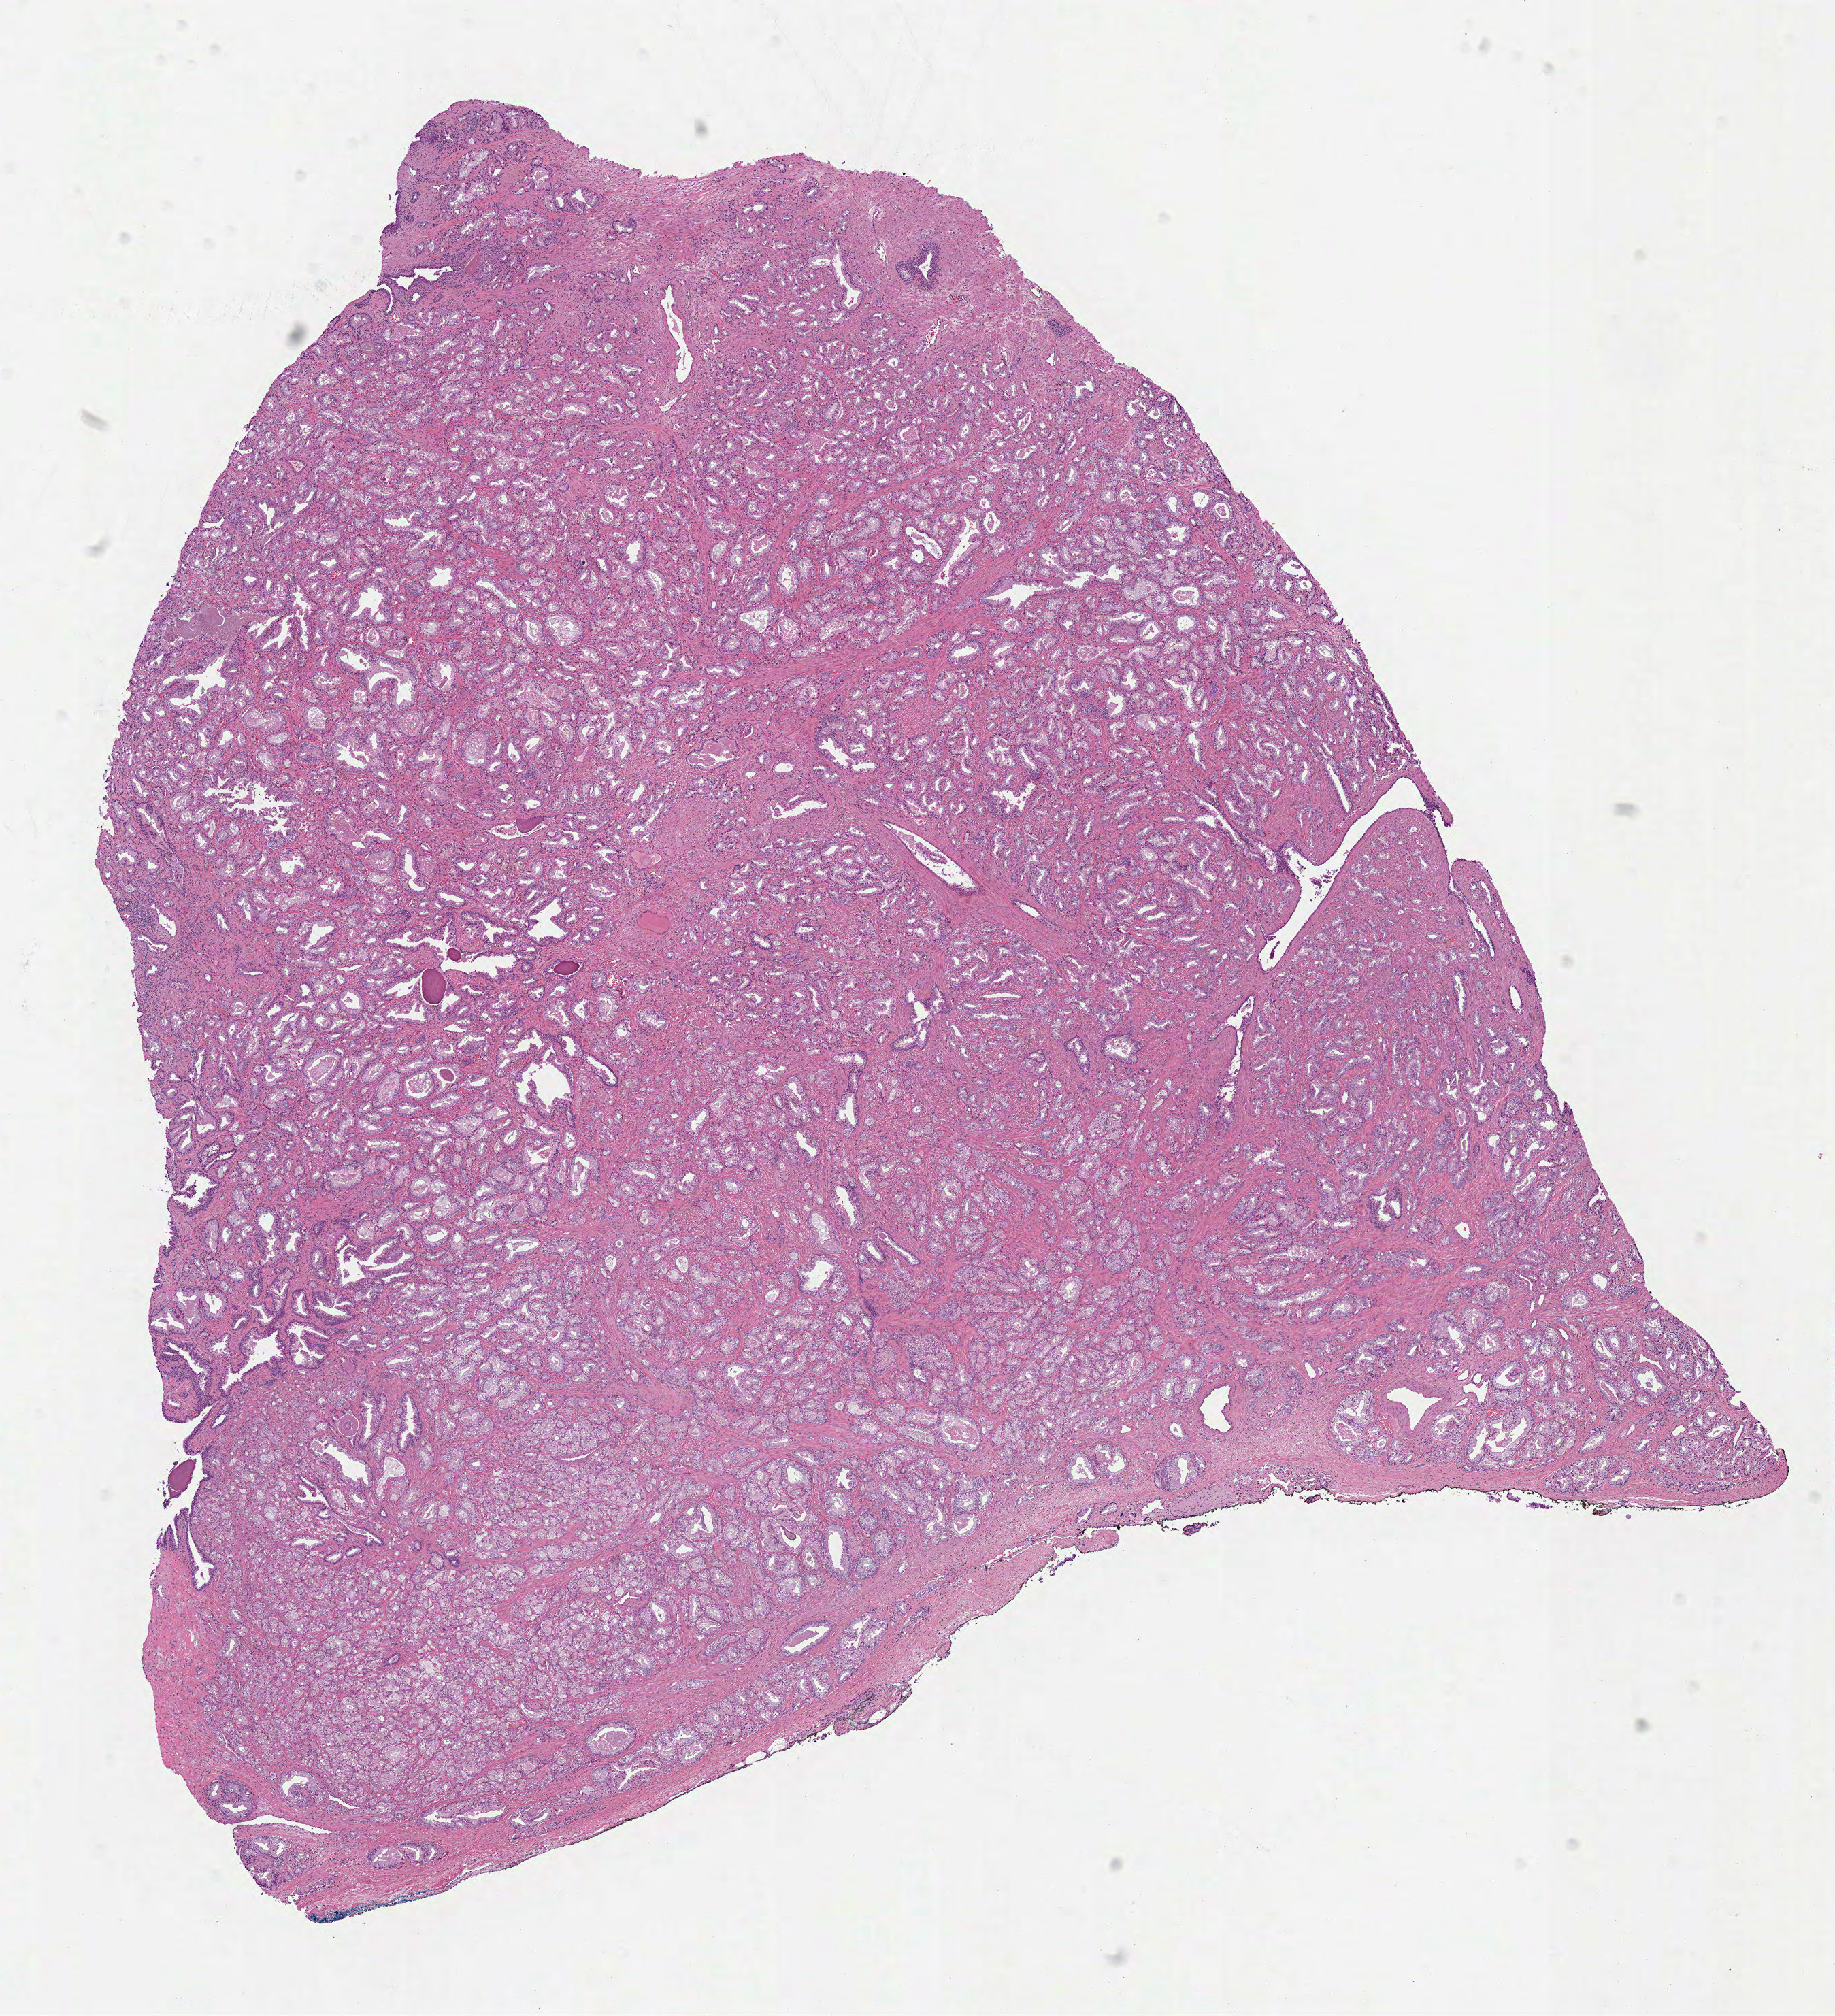
Whole-slide histology image, Hematoxylin and eosin (H&E) stained — a low-resolution overview of the entire scanned area, about 10.9 x 12.0 mm (acquisition: 40x scan). Formalin-fixed paraffin-embedded (FFPE) diagnostic section. Primary tumour sample from the prostate. Patient: male, age at initial diagnosis 59 years. Gleason score: 7 (3+4).
Laterality: bilateral. Diagnosis: Acinar cell carcinoma. Lymph nodes positive (case pathology): 0 of 13 examined.